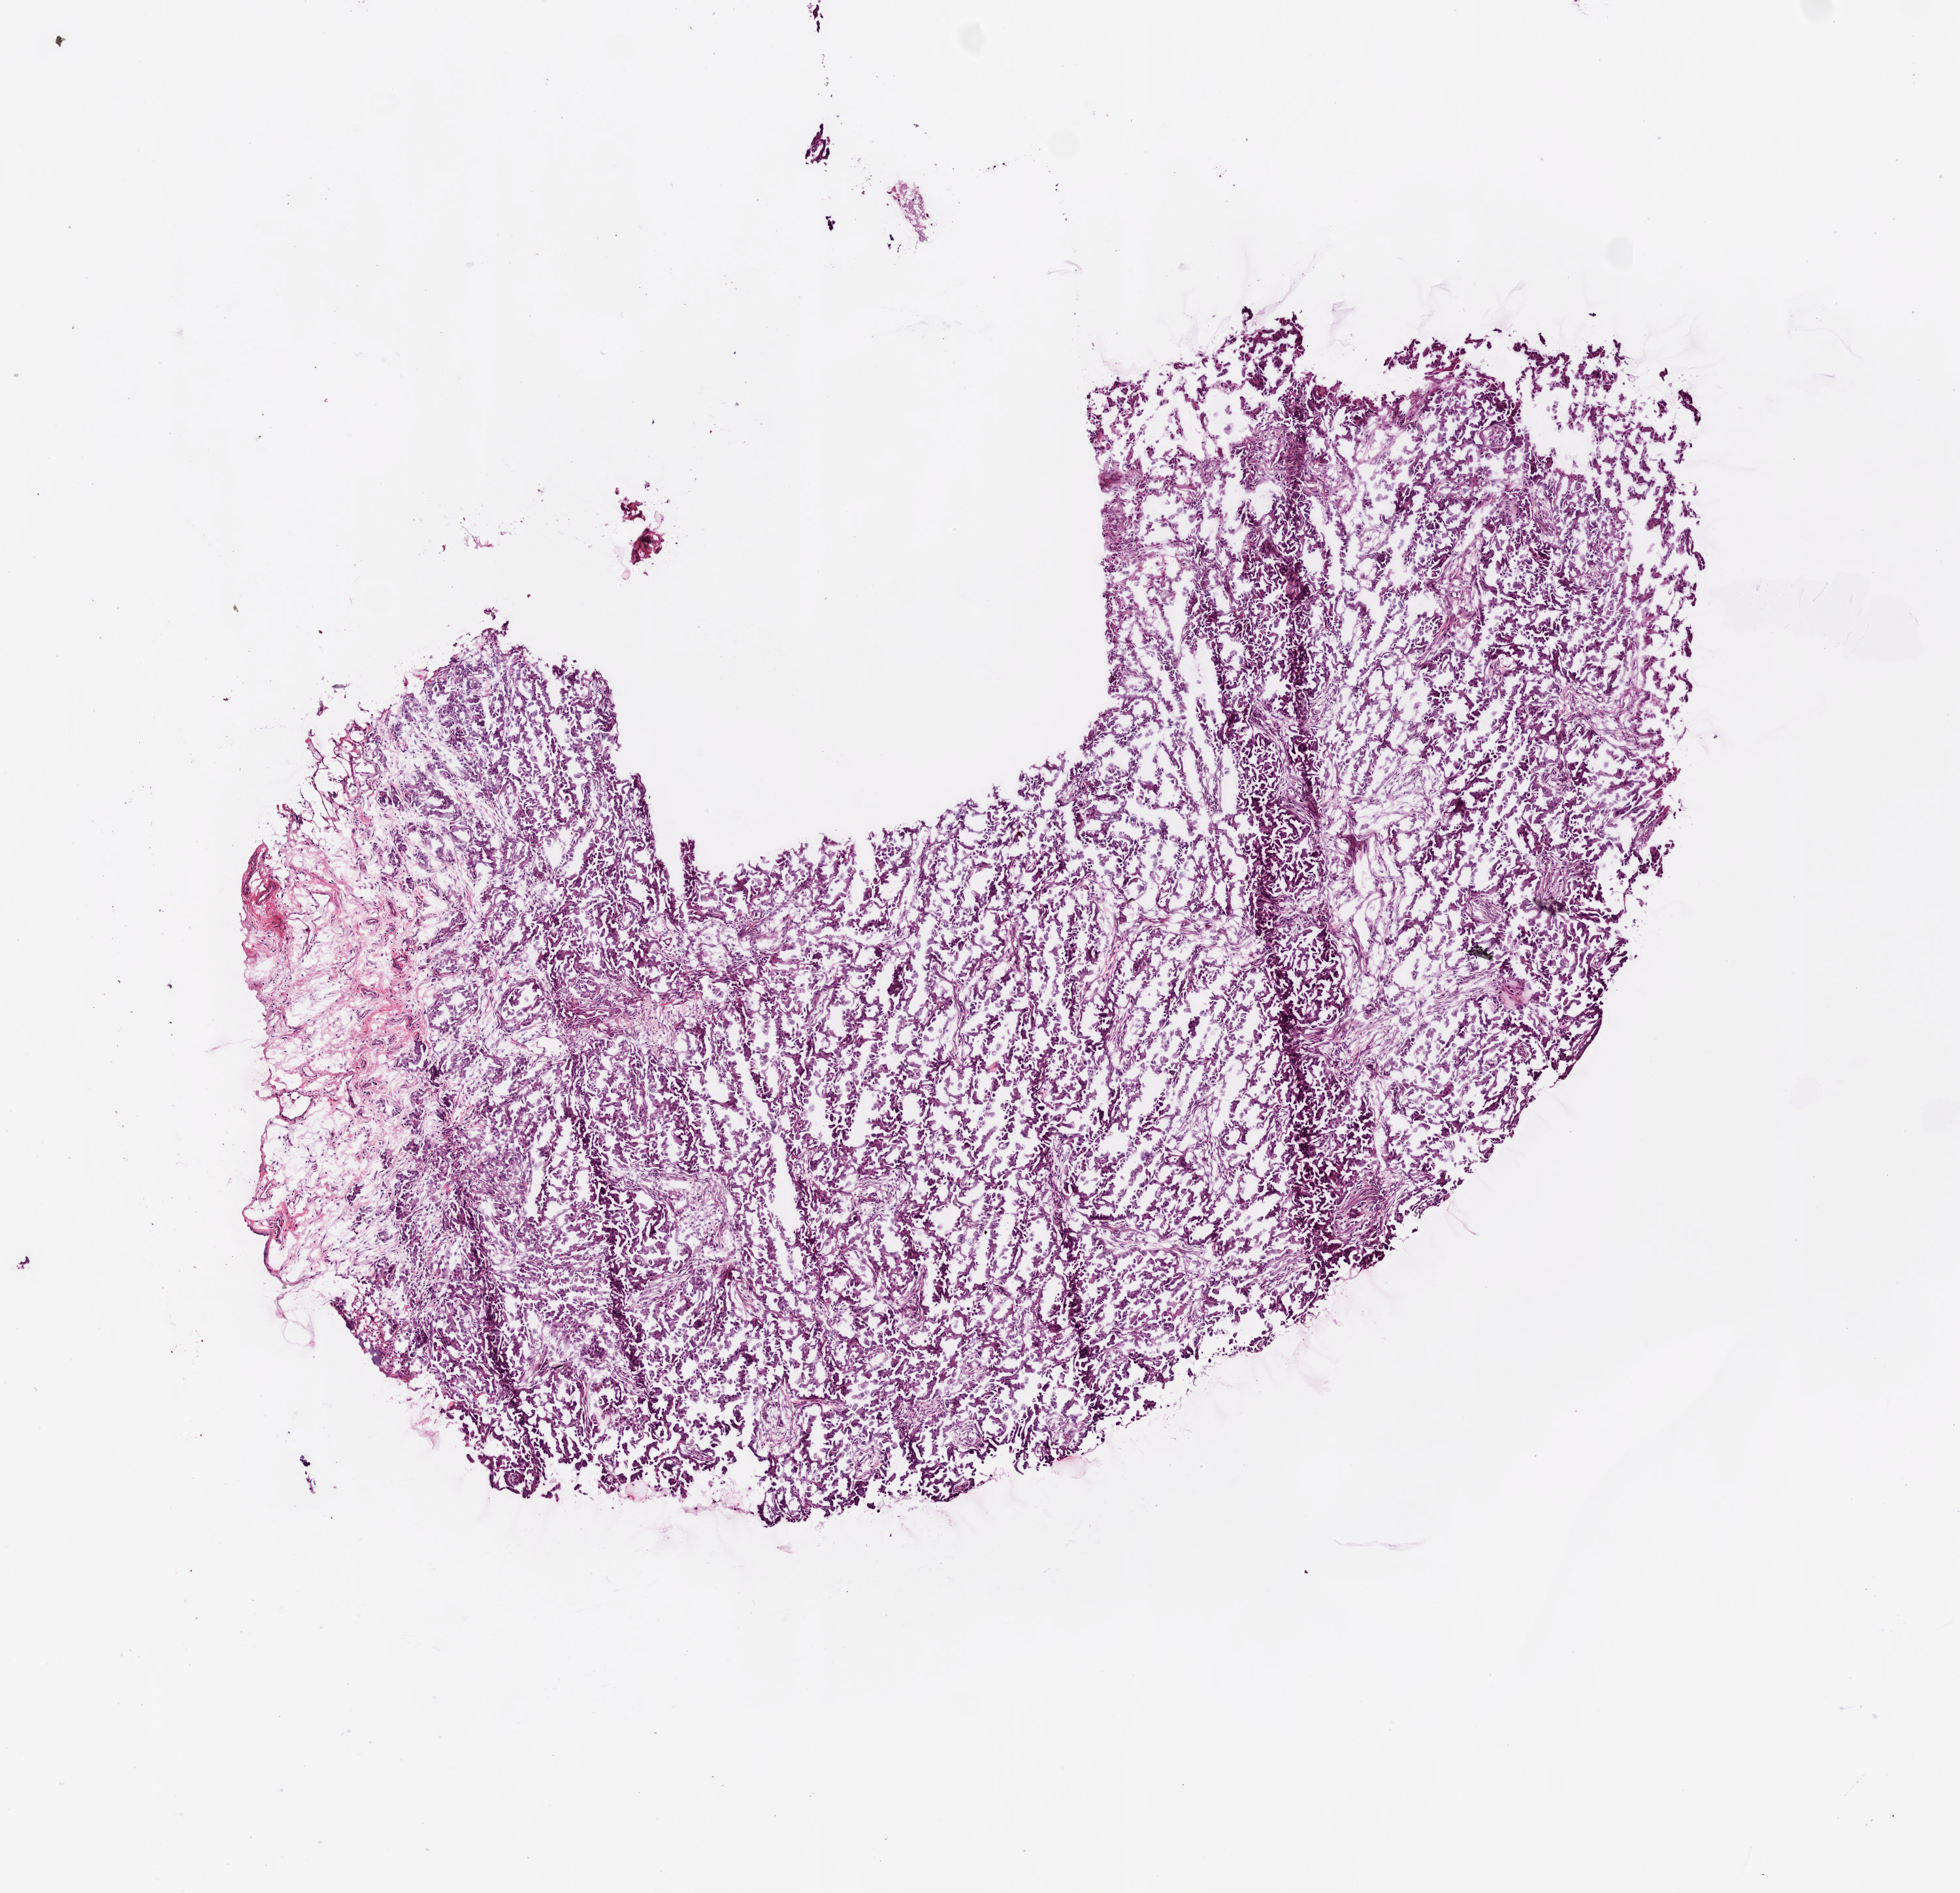
Whole-slide histology image, H&E-stained — low-resolution overview of the scanned area, about 6.0 x 5.8 mm; frozen section; ovary, recurrent tumour sample. Female patient; age at initial diagnosis 54 years. Composition of this section per pathologist review: tumour cells 90%, tumour nuclei 95%, normal cells 0%, stromal cells 10%, necrosis 0%.
- this section: recurrent tumour
- patient diagnosis: Serous cystadenocarcinoma, NOS